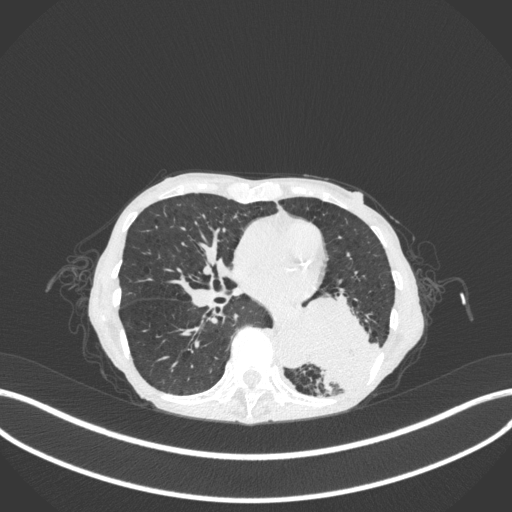
Chest CT, one axial slice; position 128 of 347 along the scan axis; reconstruction kernel B31f; lung window (W 1500 / L -600 HU); 512 × 512 image matrix, field of view 400 × 400 mm. Patient: female, 70 years. Case-level facts recorded for this patient, not image findings: clinical TNM (as recorded): T3 N0 M0.
Outlined on this slice (rectangle marked by the reading radiologist):
- lung tumour (recorded histology: small cell carcinoma): bounding box [x1, y1, x2, y2] px = [289, 285, 380, 394]